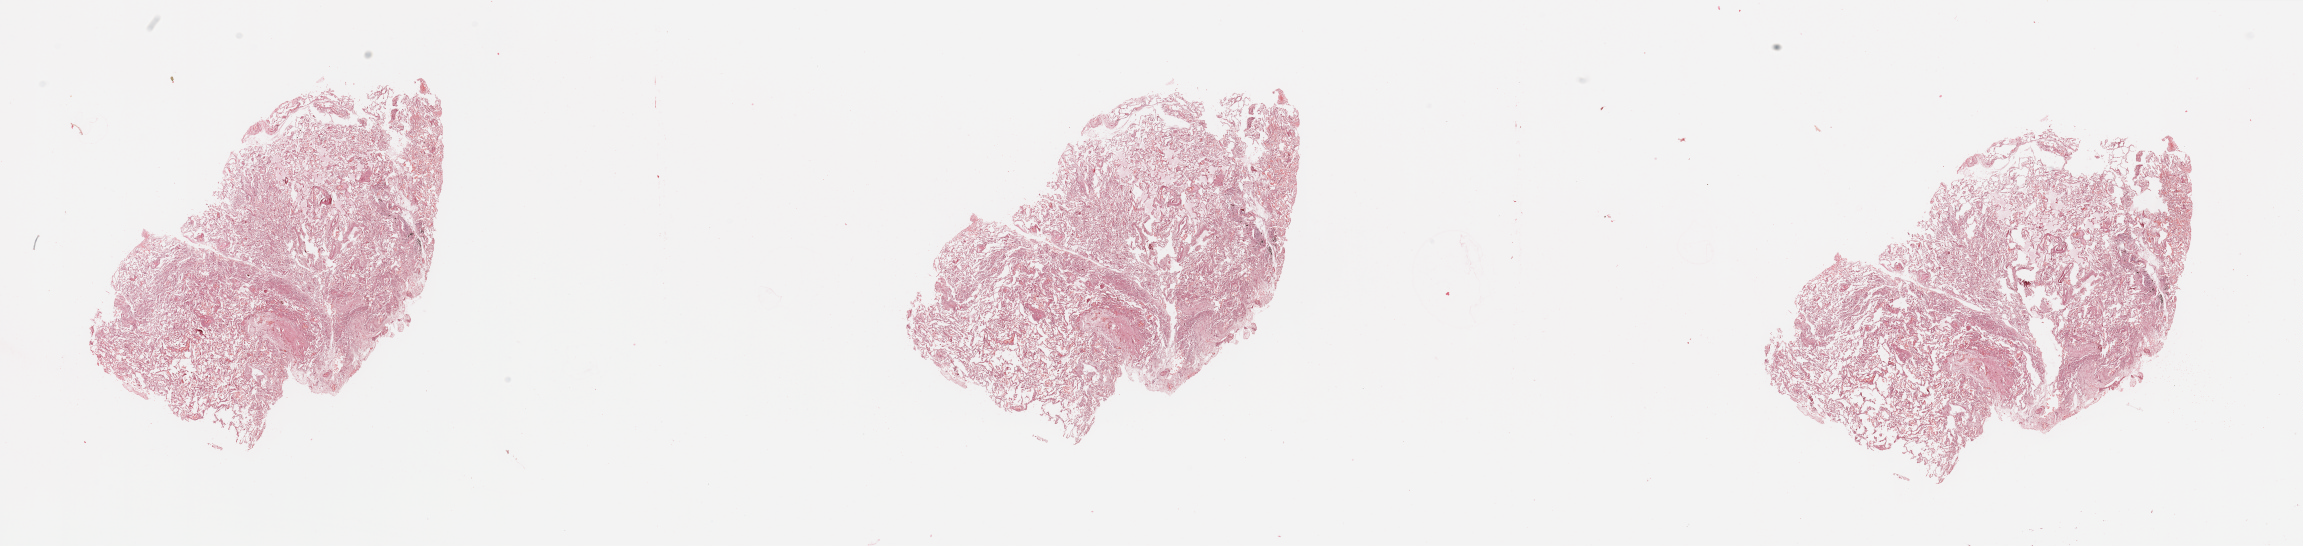
Whole-slide histology image, H&E-stained, whole scanned area (about 36.4 x 8.6 mm) shown as a low-resolution overview. Normal (non-tumour) tissue sample, lung. 71-year-old male patient.
This section: normal (non-tumour) tissue from the same patient. Patient diagnosis (cohort enrolment): squamous cell carcinoma (lung).